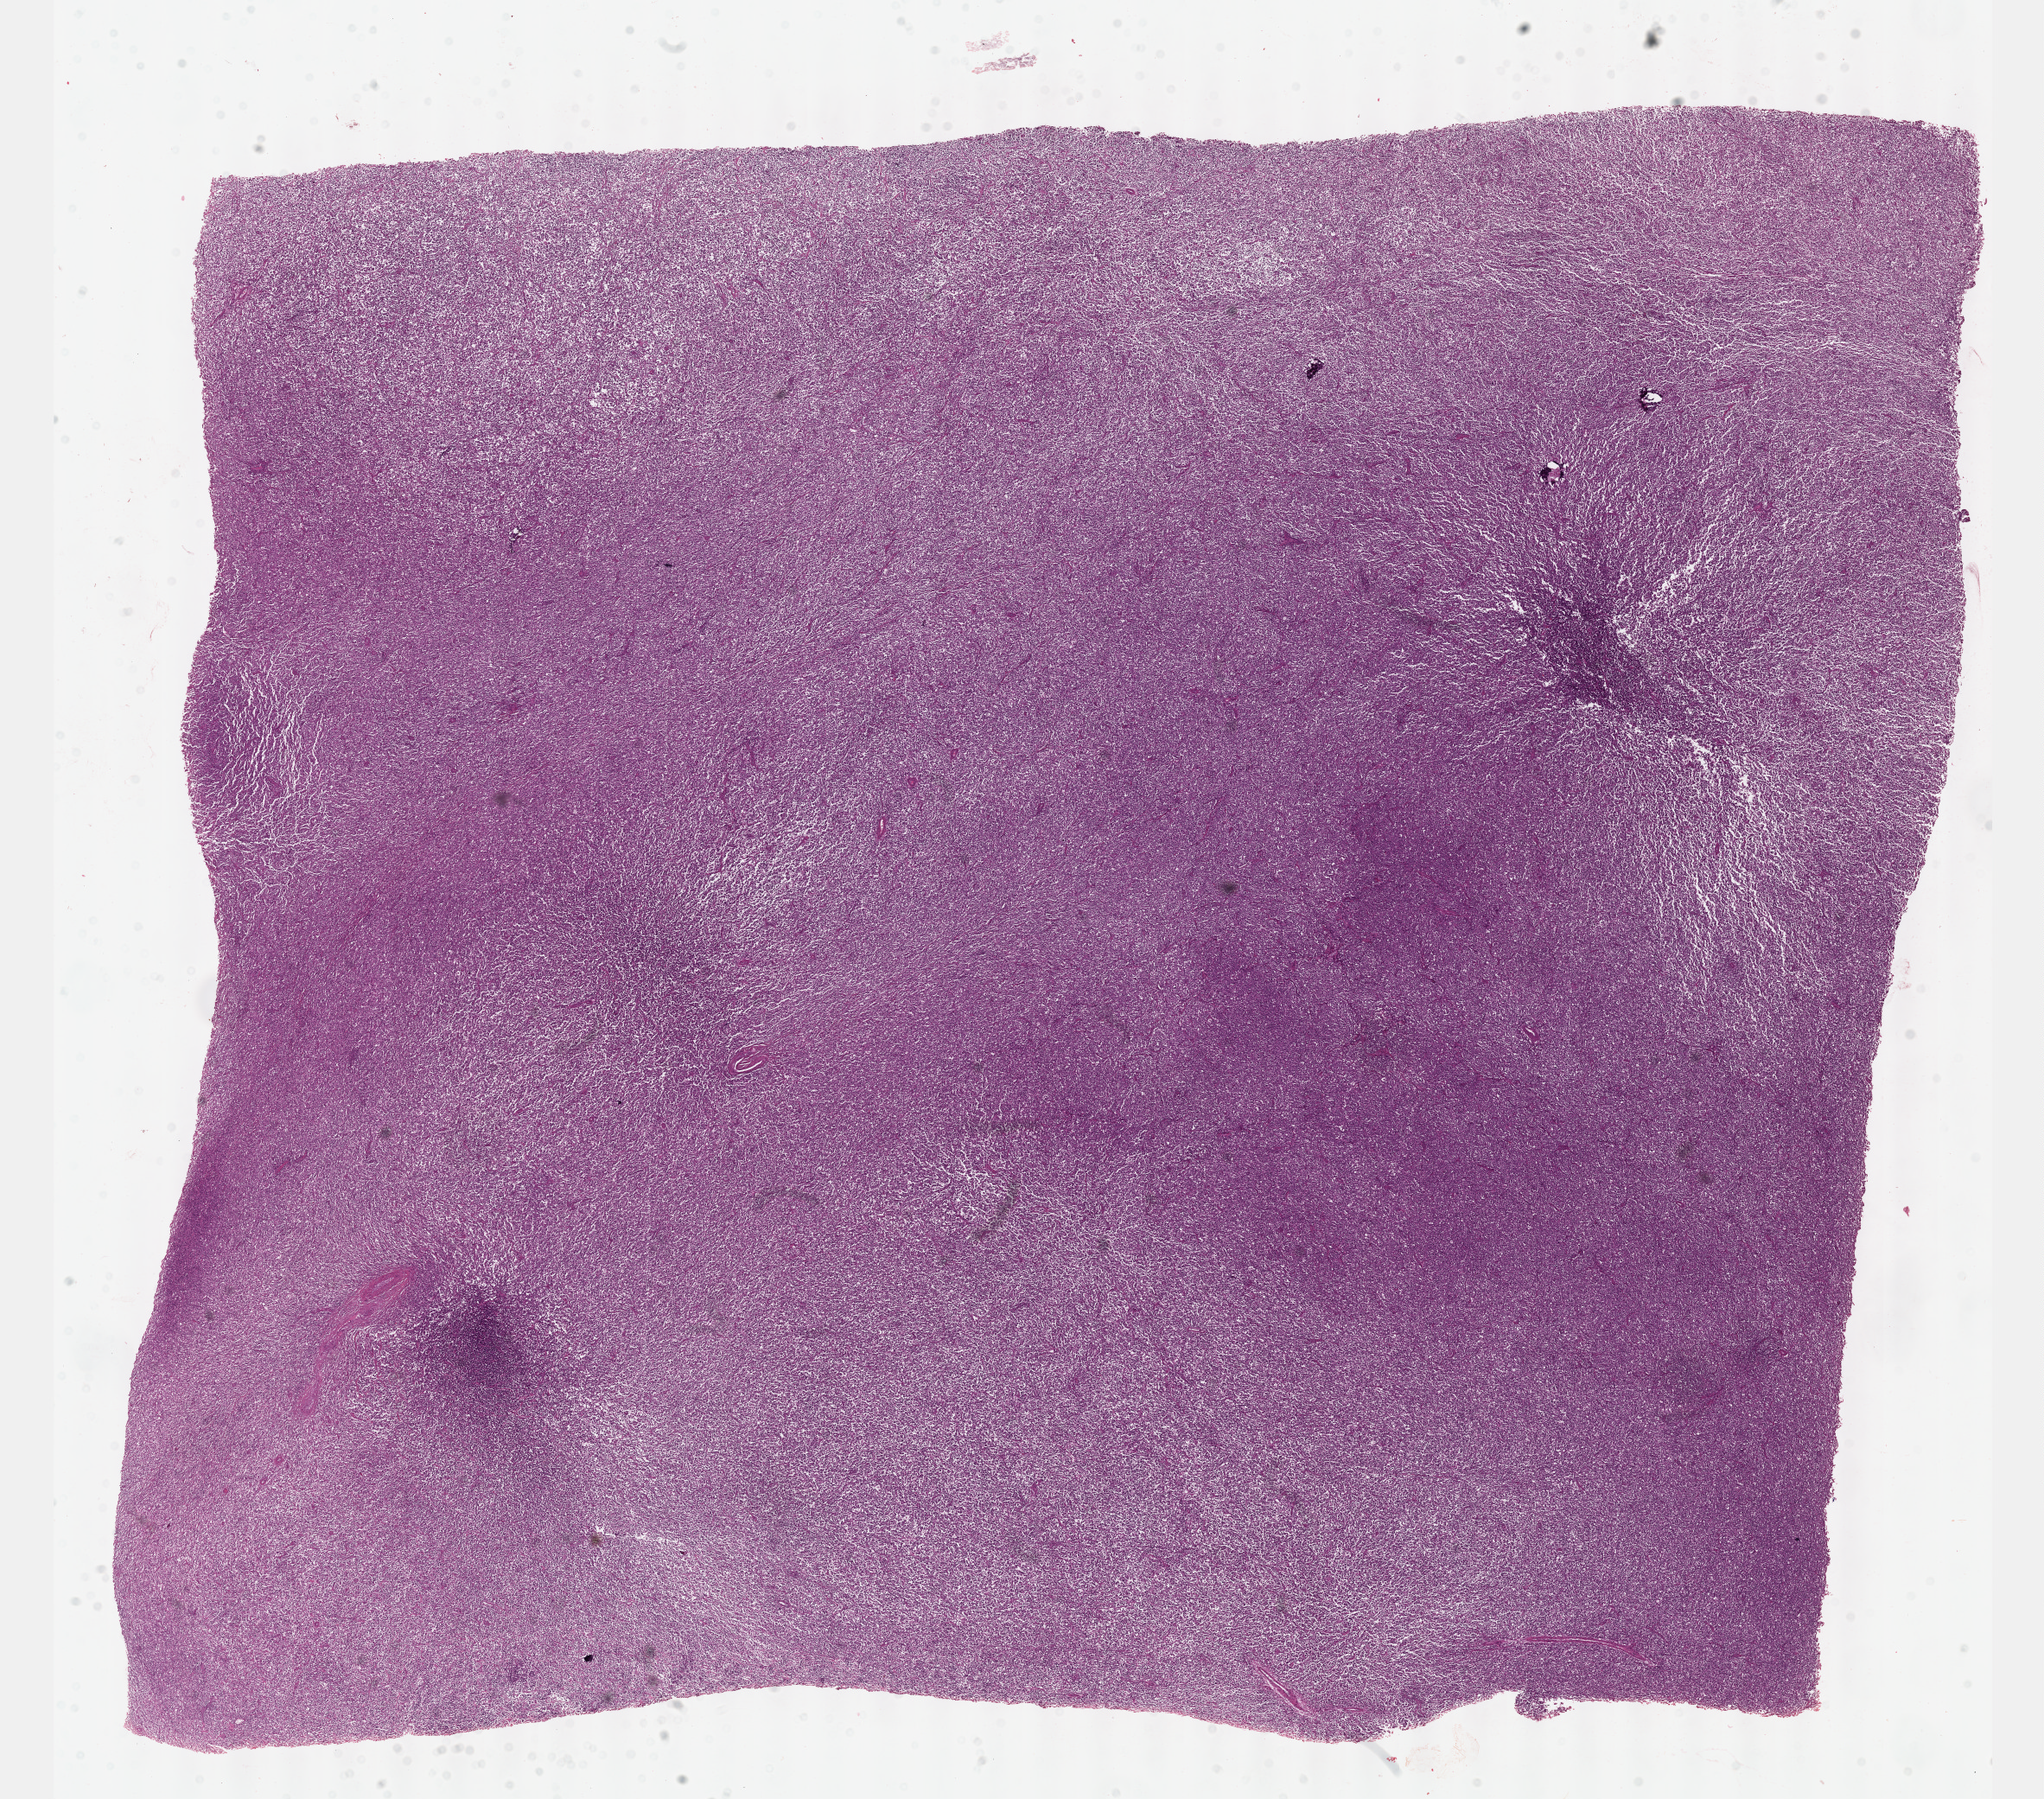
H&E whole-slide image, low-resolution overview of the scanned area, about 19.1 x 16.8 mm (slide scanned at 40x), formalin-fixed paraffin-embedded (FFPE) diagnostic section, lymphoid tissue, primary tumour sample. Female patient.
Histologic diagnosis: Diffuse large B-cell lymphoma, NOS (lymph nodes of axilla or arm).